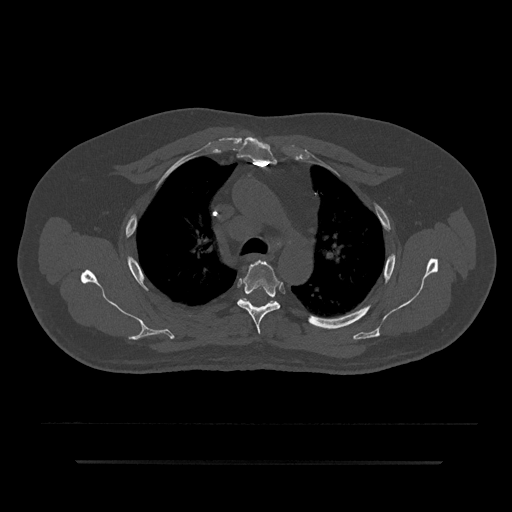
CT including the spine, one axial slice; slice 613 of 797 in the series (ordered by position); 120 kVp; bone window (W 1800 / L 400 HU); 512 × 512 image matrix. Male patient, age 59 years. Case-level facts recorded for this patient, not image findings: primary cancer: bile ducts; vertebrae with lytic lesions (as recorded): T10.
Outlined on this slice (semi-automatically segmented with operator editing):
- T4 vertebra: box from (x=237, y=260) to (x=283, y=334) px
- T5 vertebra: (x=237, y=298)–(x=279, y=304)